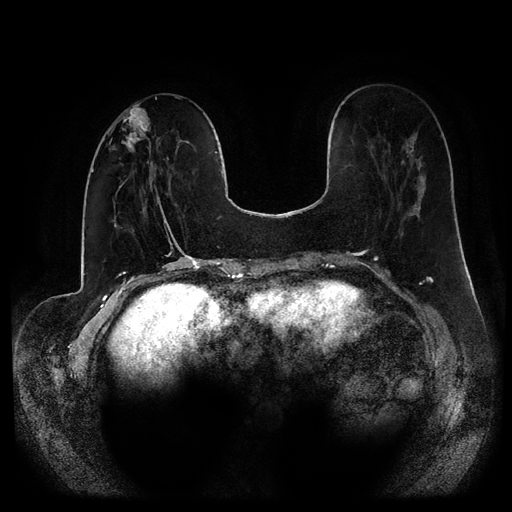
Breast MRI (dynamic contrast-enhanced, multi-phase), one axial slice. Slice 32 of 116 in the series (ordered by position). Dynamic contrast-enhanced series, time point 2 of 5 at this slice position (early post-contrast). 1.5 T. TE 2.6 ms, TR 5.2 ms. 512 × 512 image matrix, field of view 380 × 380 mm. Female patient, age 53 years.
Annotated regions visible in this slice (semi-automatic segmentation, software-assisted and operator-edited):
- breast lesion (labelled 'tumour' in the annotation; benign lesions carry a separate 'benign' label): box from (x=121, y=104) to (x=151, y=152) px